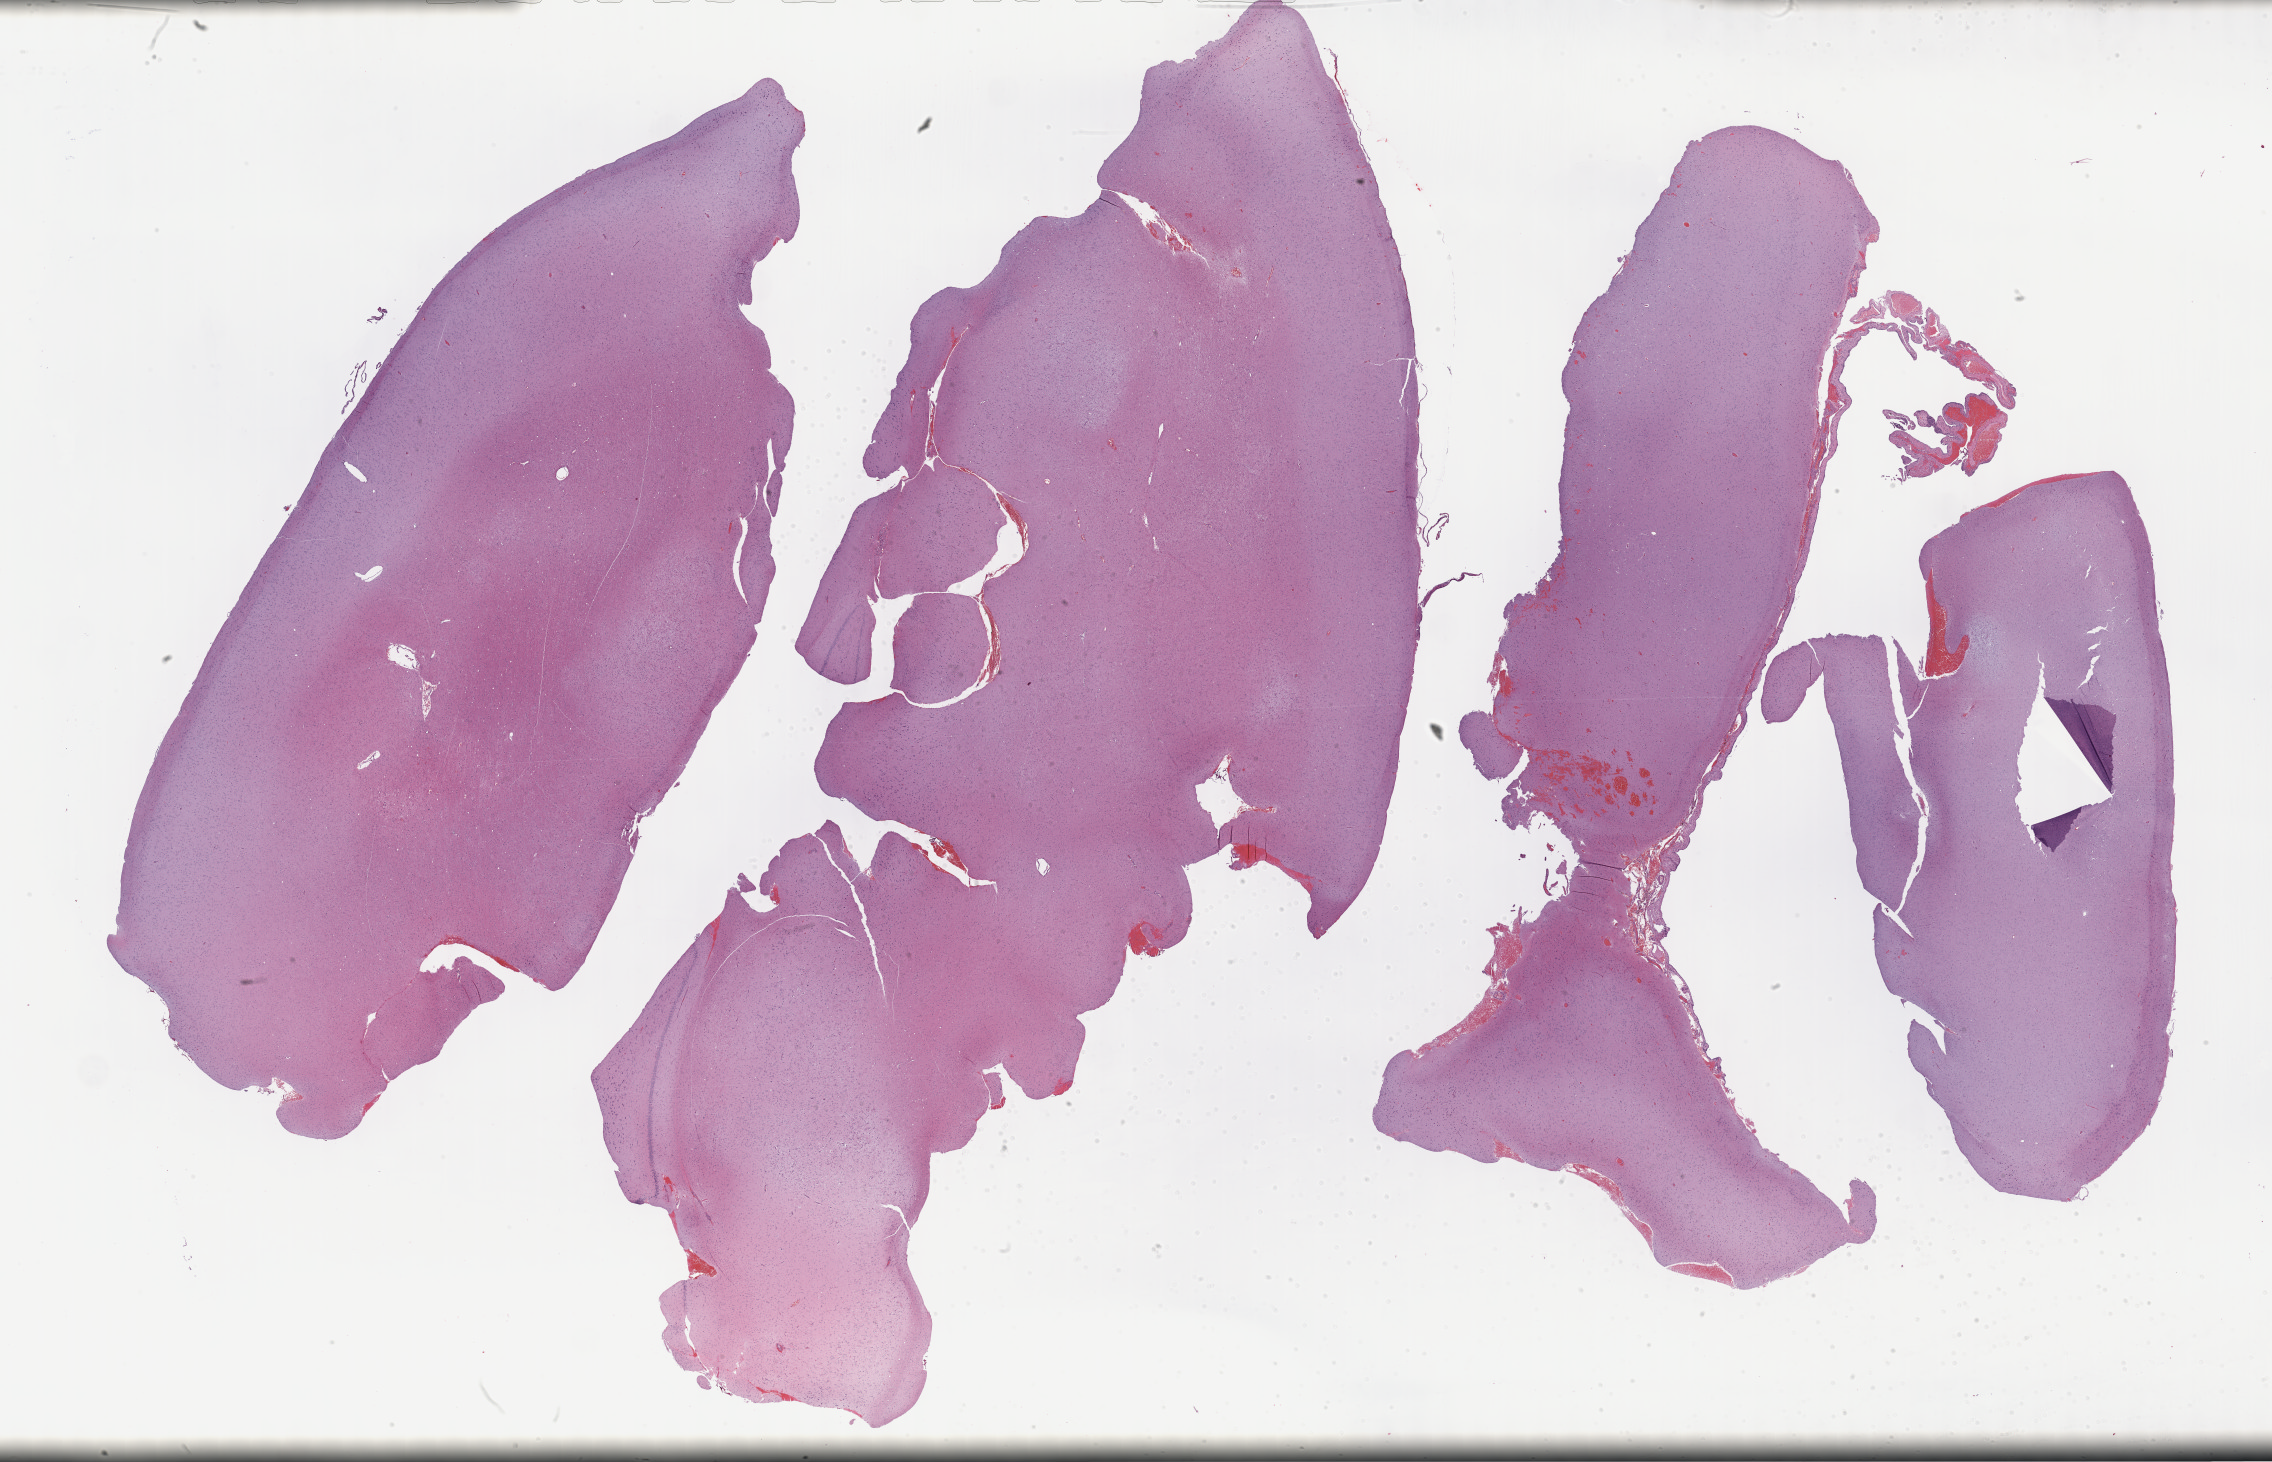
Whole-slide histology image, H&E, low-resolution overview of the scanned area, about 36.7 x 23.6 mm (slide scanned at 40x), formalin-fixed paraffin-embedded (FFPE) diagnostic section, primary tumour sample from the brain. Female patient; age at initial diagnosis 37 years. Histologic grade: G2 (moderately differentiated).
Diagnosis: Astrocytoma, NOS (cerebrum). Laterality: left.